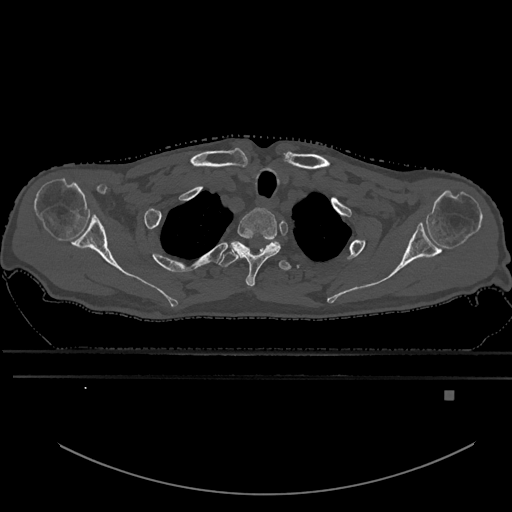
CT including the spine, one axial slice. Position 522 of 969 along the scan axis. Bone window (W 1800 / L 400 HU). 0.5 mm slice thickness. 512 × 512 image matrix, field of view 456 × 456 mm. Patient: male, 82 years. Case-level facts recorded for this patient, not image findings: primary cancer: prostate; vertebrae with lytic lesions (as recorded): T11, T9, T8, T2.
Outlined on this slice (semi-automatic segmentation, software-assisted and operator-edited):
- T1 vertebra: bounding box (x1, y1, x2, y2) in pixels: (232, 208, 281, 288)
- T2 vertebra: (219, 238, 280, 267)